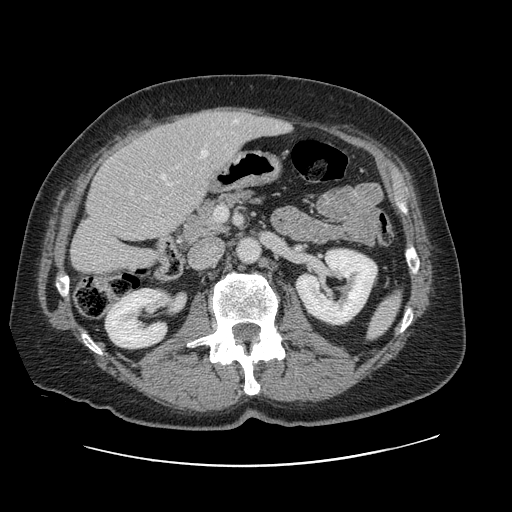
Contrast-enhanced abdominal CT, one axial slice. Position 39 of 138 along the scan axis. 120 kVp. Intravenous contrast given. Soft-tissue window (W 400 / L 40 HU). 512 × 512 image matrix. Male patient, age 71 years. From the clinical record (not read from this slice): diagnosis: colorectal cancer liver metastases, imaged before liver resection; multiple liver metastases: no; largest metastasis: 3.3 cm; disease in both lobes: no.
Annotated regions visible in this slice (manually delineated by an expert):
- hepatic veins: bounding box [x1, y1, x2, y2] px = [169, 120, 237, 186]
- liver: [72, 108, 287, 274]
- planned liver remnant (the part of the liver to remain after resection): [72, 133, 191, 274]
- portal vein (with intrahepatic branches): [162, 175, 166, 180]